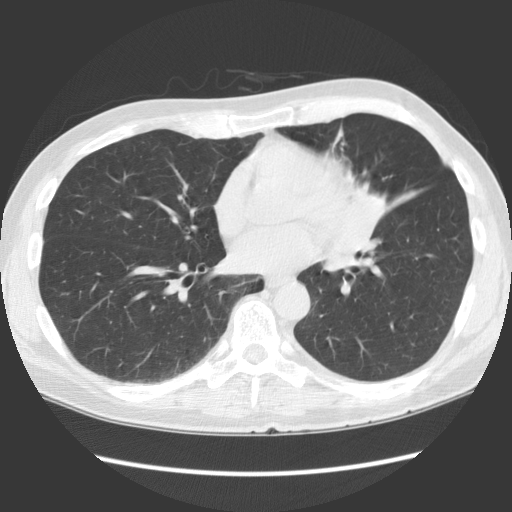
Low-dose screening chest CT, one axial slice. Position 61 of 136 along the scan axis. Reconstruction kernel STANDARD. 140 kVp. Lung window (W 1500 / L -600 HU). 512 × 512 image matrix.
Outlined on this slice (outlined manually by an expert reader):
- lesion 1 (tumor, hilum of left lung): bounding box <351,182,388,236> (left, top, right, bottom; pixels)